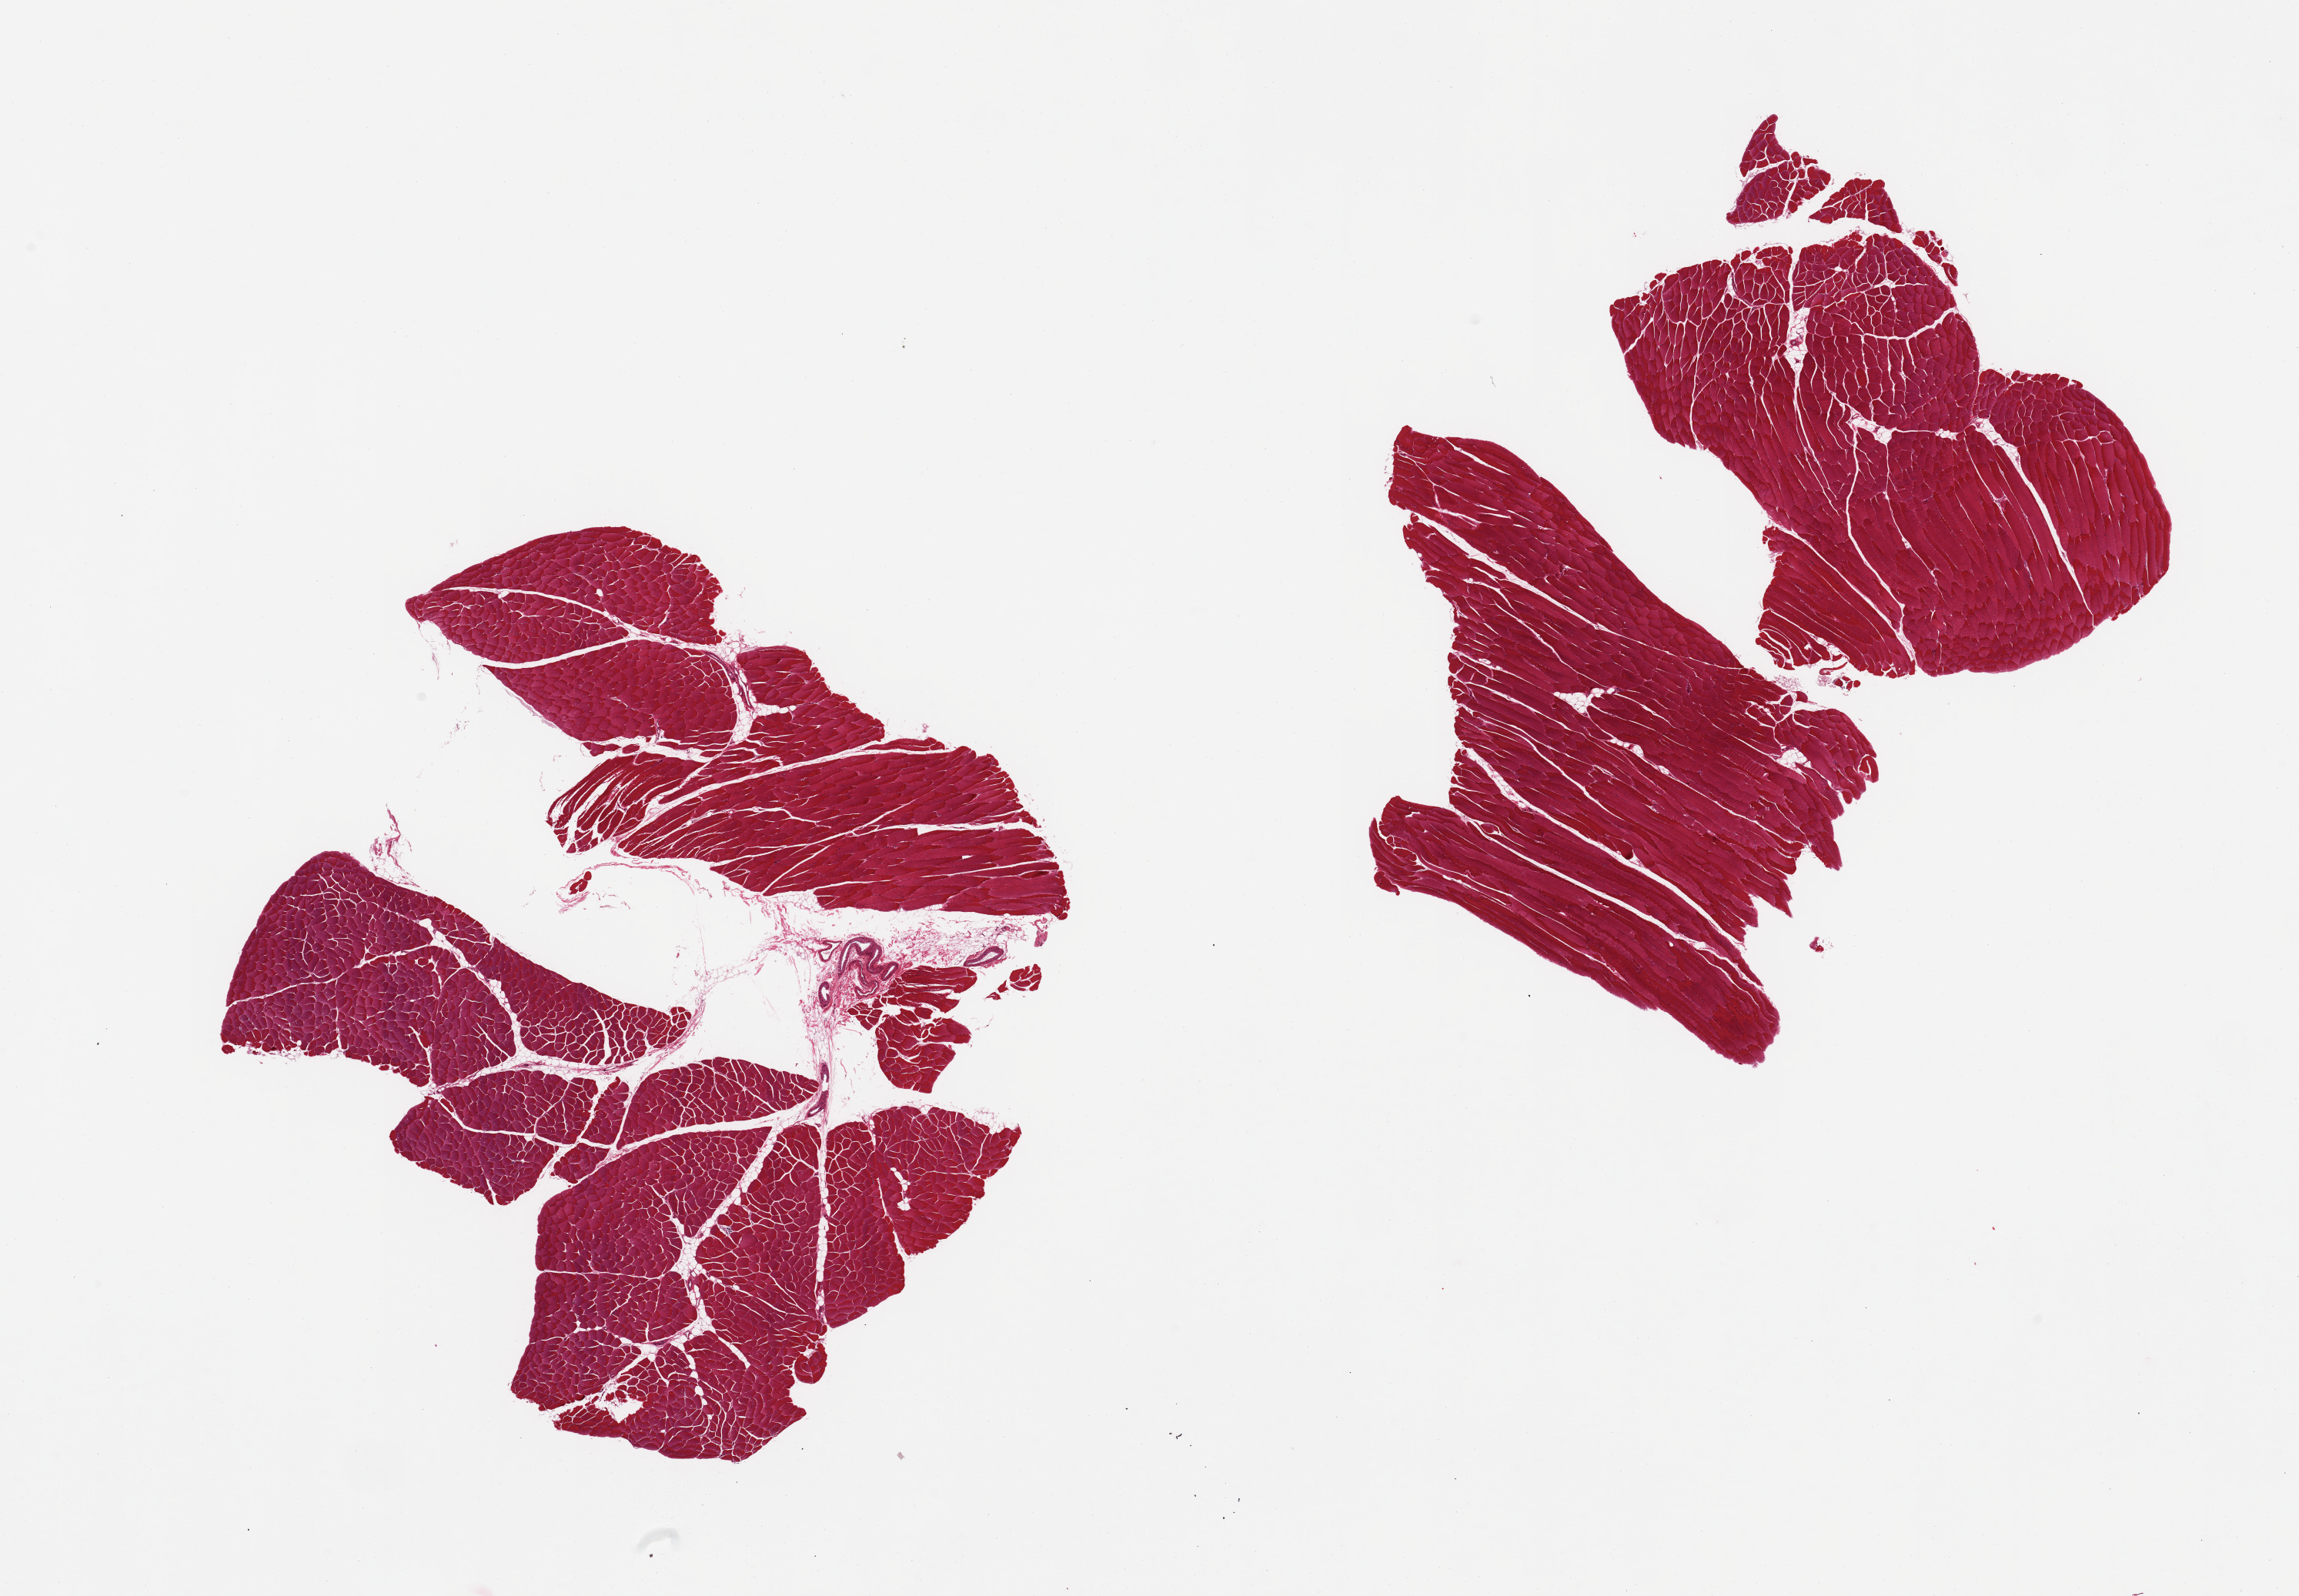
Whole-slide image, hematoxylin and eosin (H&E) stain, whole scanned area (about 23.6 x 16.4 mm, acquisition: 20x scan) shown as a low-resolution overview; PAXgene-fixed, paraffin-embedded tissue; sampled site (target tissue): skeletal muscle; tissue donor sample. Male donor.
Reviewer comment on this tissue sample: 2 pieces; well trimmed.